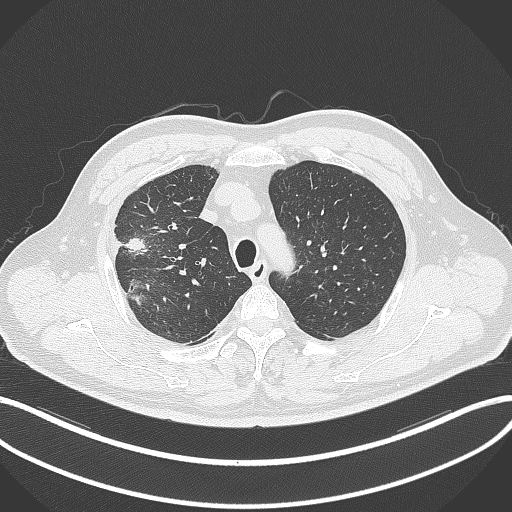
Chest CT, one axial slice. Slice 269 of 348 in the series (ordered by position). Lung window (W 1500 / L -600 HU). 1 mm slice thickness. 512 × 512 image matrix, field of view 400 × 400 mm. Patient: male, 55 years. From the clinical record (not read from this slice): clinical TNM (as recorded): T3 N2 M1.
Structures marked on this image (bounding box drawn by a radiologist):
- lung tumour (recorded histology: adenocarcinoma): bounding box <122,235,158,305> (left, top, right, bottom; pixels)